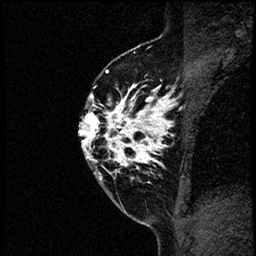
Breast MRI (dynamic contrast-enhanced), one sagittal slice; slice 40 of 60 in the series (ordered by position); dynamic contrast-enhanced study with each time point stored as its own series, time point 2 of 4 at this slice position (early post-contrast, ordered by acquisition time); 1.5 T; TE 4.2 ms, TR 17.6 ms; 2 mm slice thickness; 256 × 256 image matrix, field of view 200 × 200 mm. Female patient, age 40 years. From the clinical record (not read from this slice): setting: breast cancer imaged before/during neoadjuvant chemotherapy; receptor status: HER2-positive.
Structures marked on this image (semi-automatically segmented with operator editing):
- analysis volume of interest (the breast-tissue region the enhancement analysis was run in; not a lesion): bounding box [x1, y1, x2, y2] px = [80, 56, 197, 205]
- tumour enhancement mask (voxels above the 100 % enhancement threshold inside the analysis volume of interest): [80, 67, 197, 180]